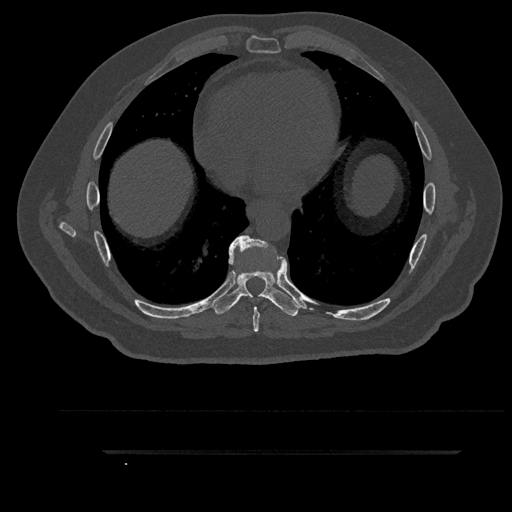
CT including the spine, one axial slice; reconstruction kernel Br40s/3; 120 kVp; bone window (W 1800 / L 400 HU); 512 × 512 image matrix, field of view 432 × 432 mm. Male patient, age 63 years. Case-level facts recorded for this patient, not image findings: primary cancer: renal; vertebrae with lytic lesions (as recorded): T8.
Outlined on this slice (semi-automatically segmented with operator editing):
- T6 vertebra: bounding box [x1, y1, x2, y2] px = [249, 293, 253, 297]
- T7 vertebra: [230, 236, 286, 332]
- T8 vertebra: [211, 244, 302, 316]